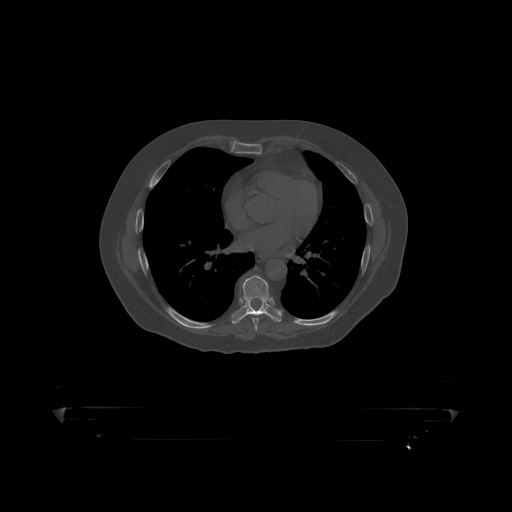
CT including the spine, one axial slice. Position 263 of 390 along the scan axis. Bone window (W 1800 / L 400 HU). 1.25 mm slice thickness. 512 × 512 image matrix. Patient: male, 60 years. From the clinical record (not read from this slice): primary cancer: prostate.
Annotated regions visible in this slice (semi-automatically segmented with operator editing):
- T8 vertebra: bounding box [x1, y1, x2, y2] px = [233, 276, 282, 318]